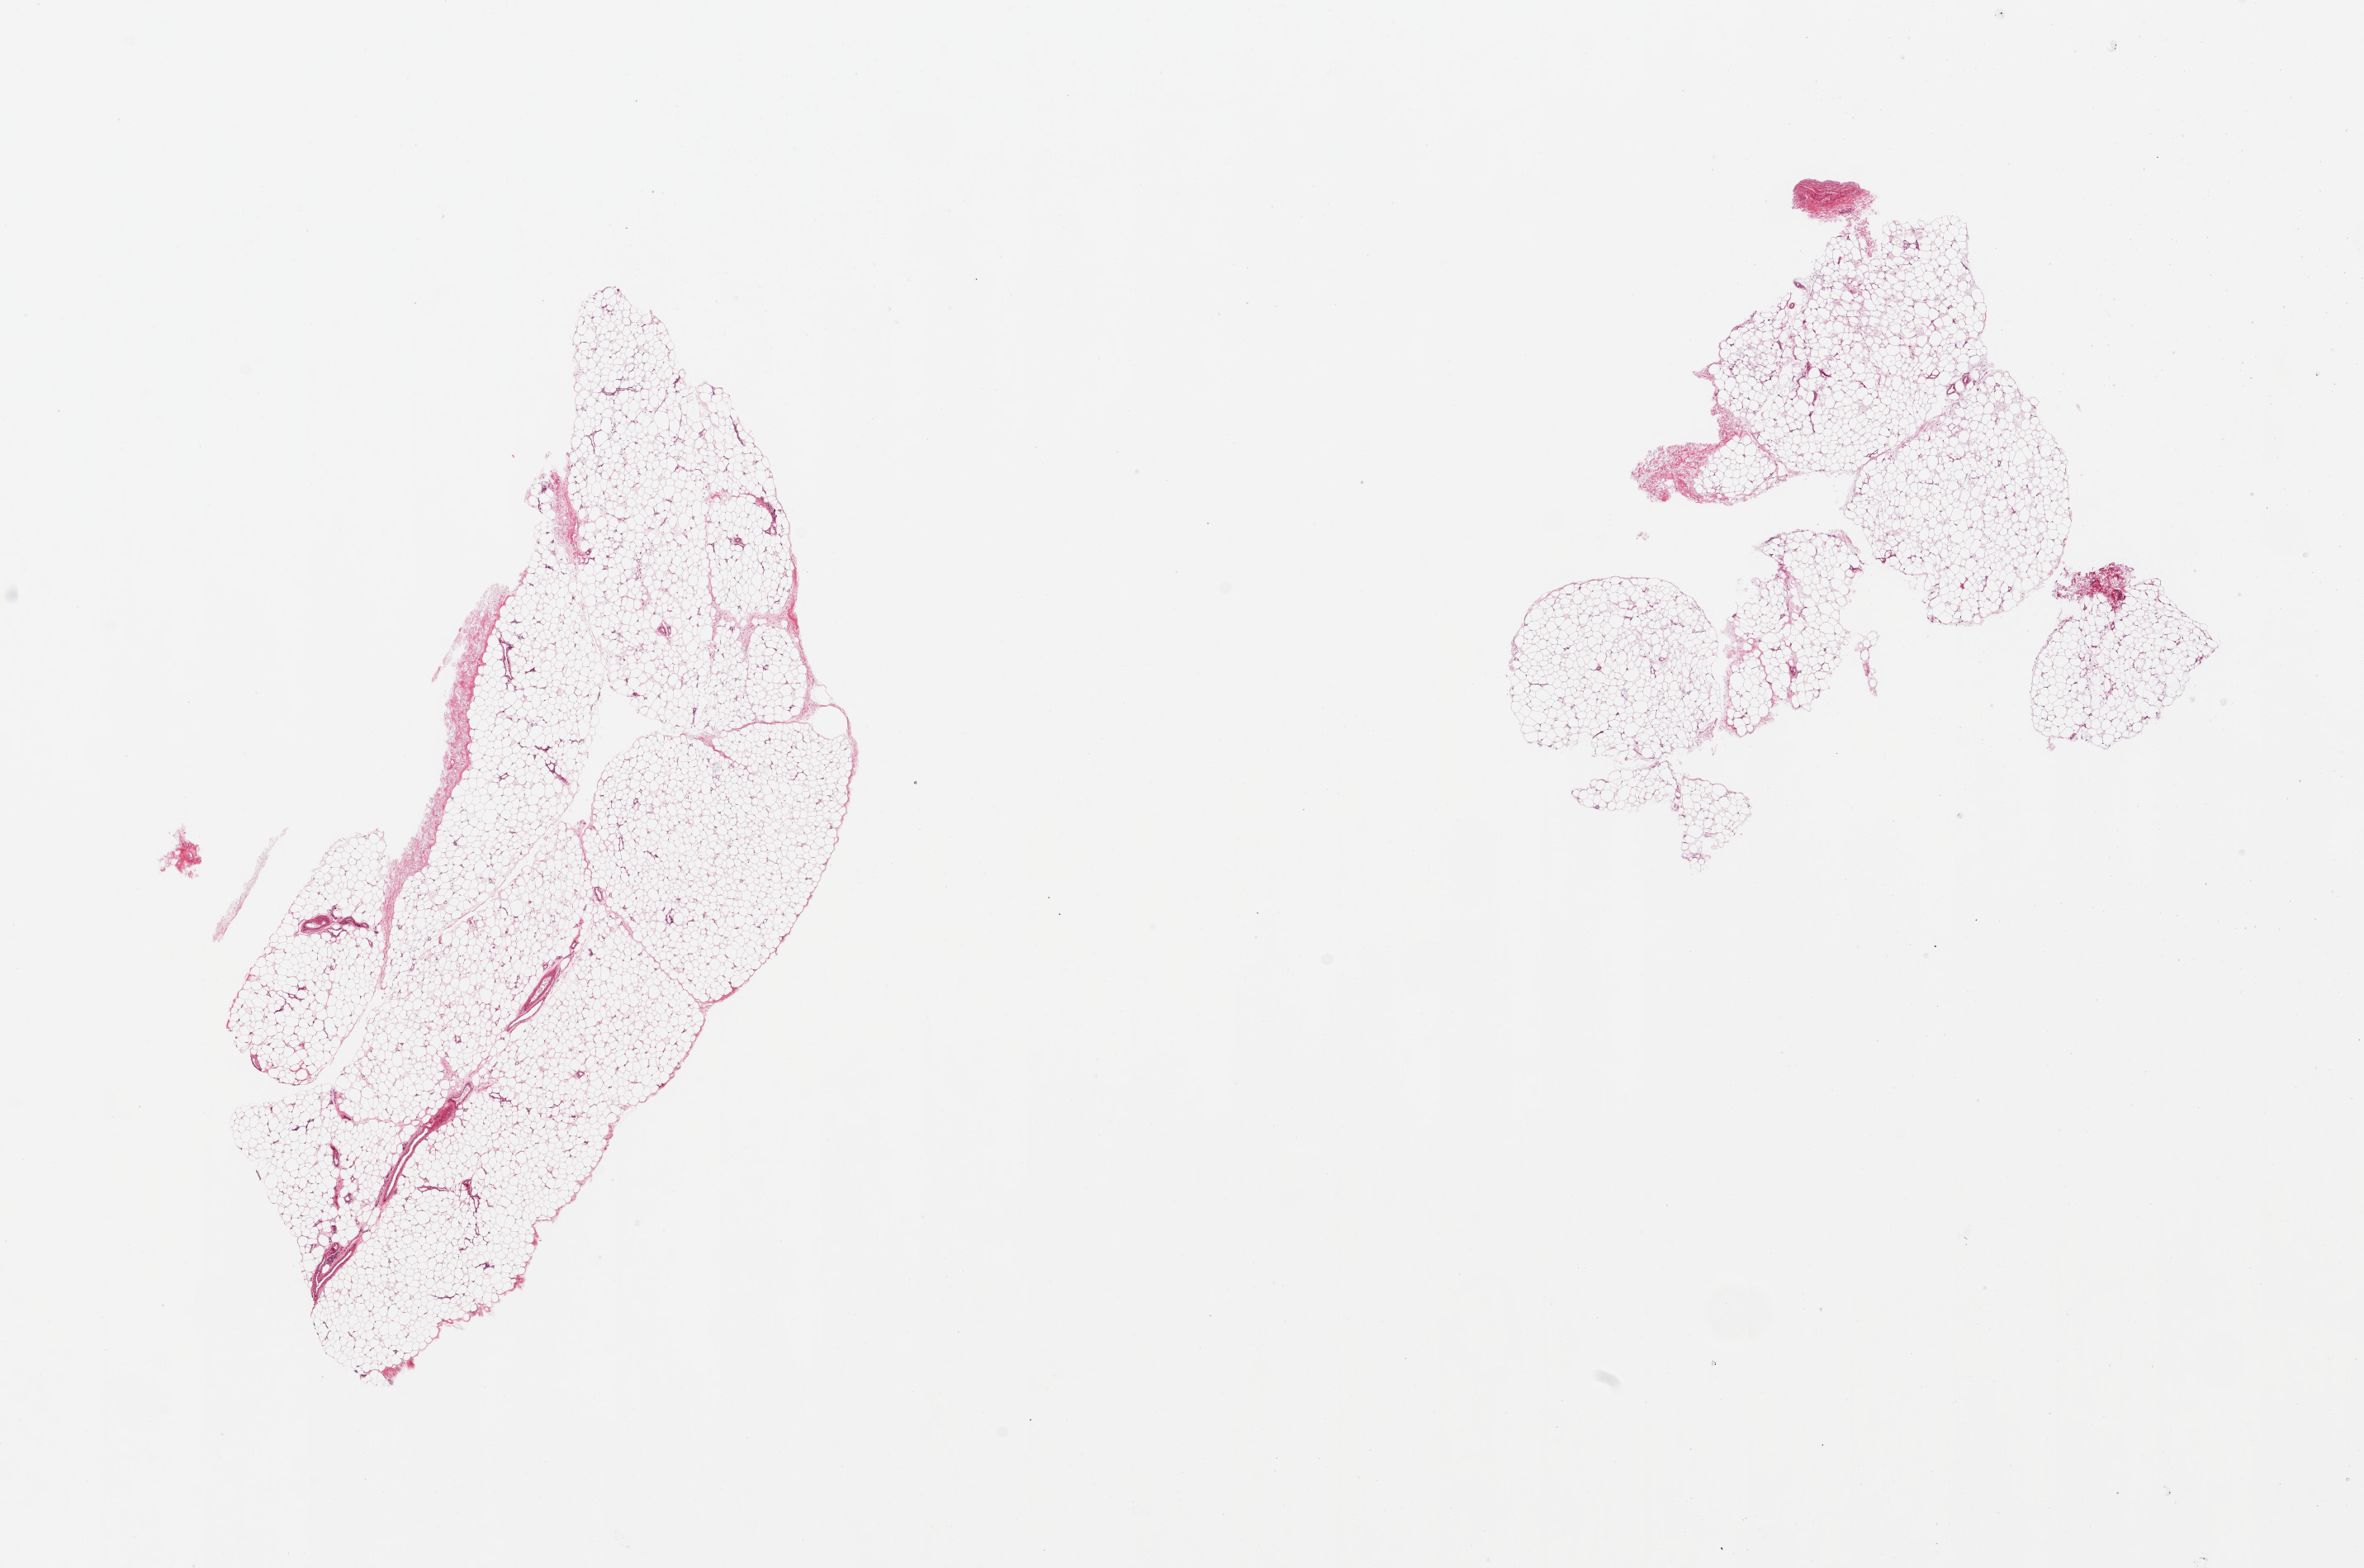
Hematoxylin and eosin (H&E) whole-slide image — shown as a low-resolution overview of the whole scanned area (about 22.6 x 15.0 mm). PAXgene-fixed, paraffin-embedded tissue. Target tissue: adipose tissue. Donor tissue sample. Donor: male.
* reviewer comment on this tissue sample: 2 pieces, ~10% fibro-fascial tissue